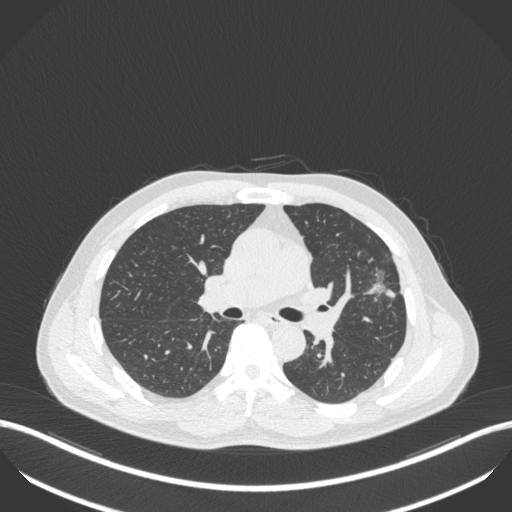
Chest CT, one axial slice; position 233 of 418 along the scan axis; reconstruction kernel B31f; 120 kVp; lung window (W 1500 / L -600 HU); 1 mm slice thickness; 512 × 512 image matrix, field of view 400 × 400 mm. Patient: male, 55 years. Case-level facts recorded for this patient, not image findings: clinical TNM (as recorded): T1c N0 M0; histopathological grade: G2-3.
Annotated regions visible in this slice (bounding box drawn by a radiologist):
- lung tumour (recorded histology: adenocarcinoma): bounding box <362,256,401,300> (left, top, right, bottom; pixels)